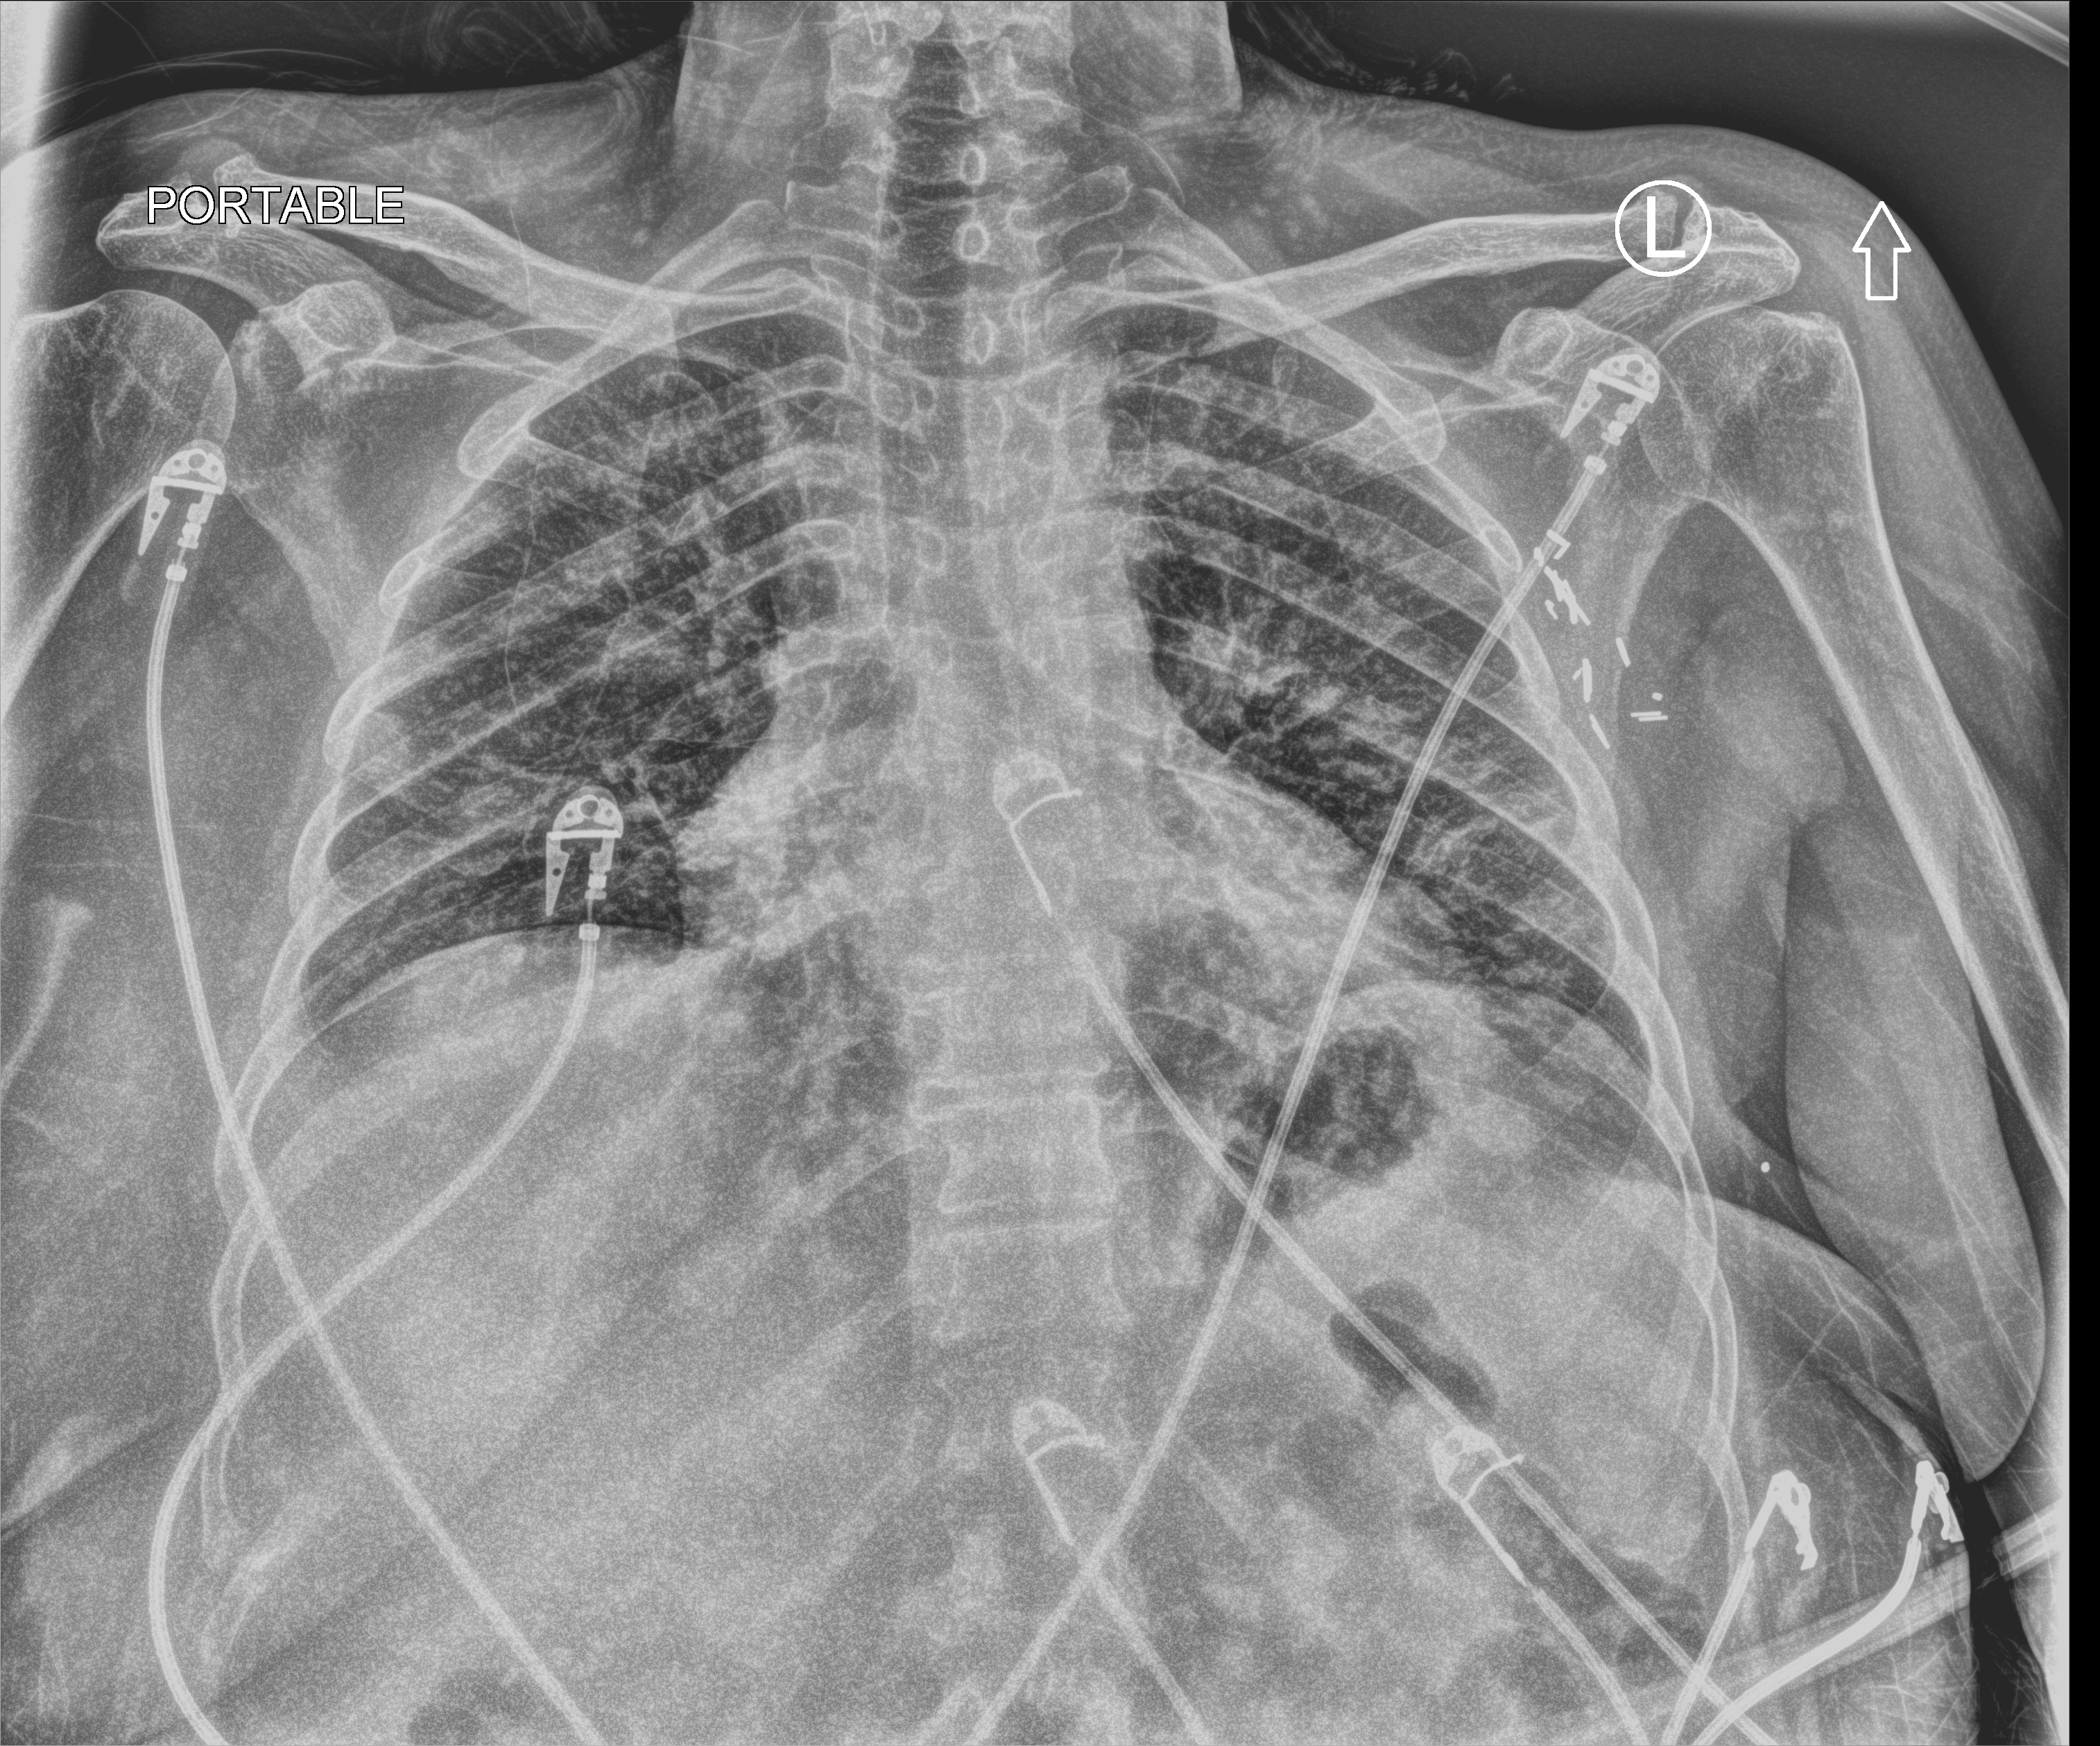
Bedside chest radiograph (computed radiography); anteroposterior (AP) projection. Patient hospitalised with COVID-19; female, aged 60–74 years.
Admission-level facts for this patient (not findings on this image; timing relative to this image not recorded):
- admitted to intensive care during this hospital stay: yes